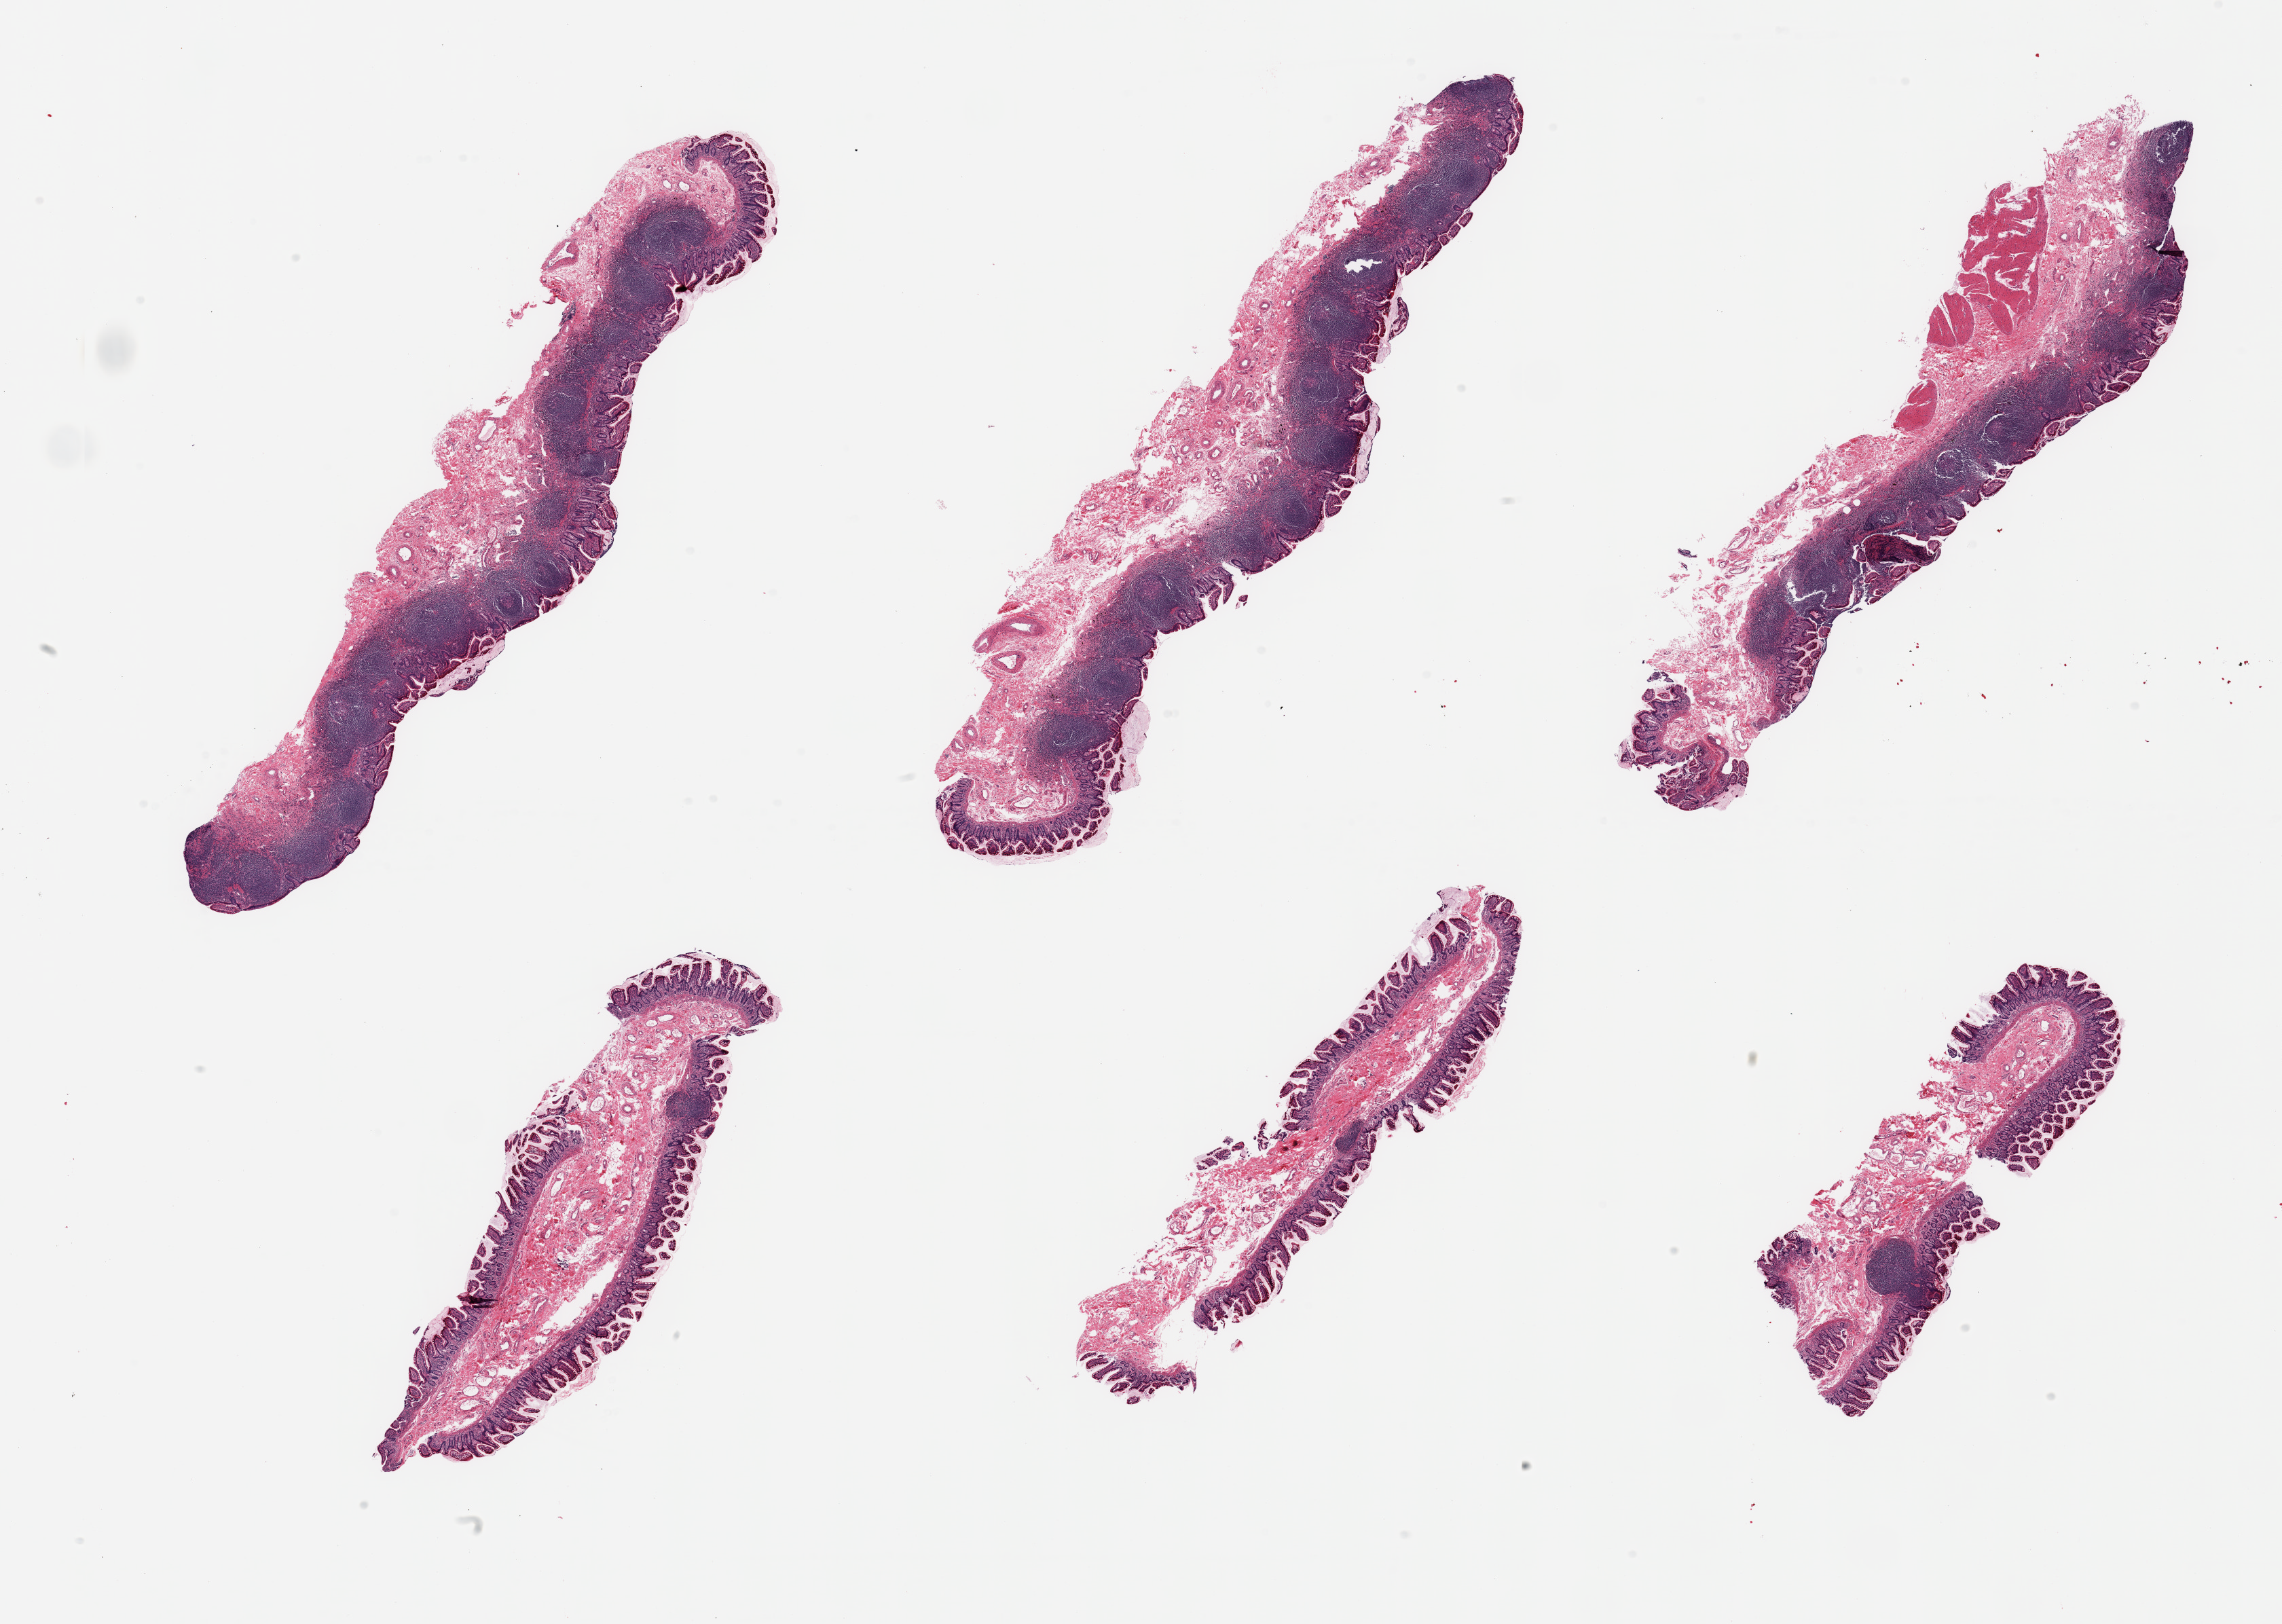
Whole-slide image, haematoxylin and eosin stain, shown as a low-resolution overview of the whole scanned area (about 26.6 x 18.9 mm); PAXgene-fixed paraffin-embedded (PFPE) section; section of ileum (target tissue); donor tissue sample. Female donor.
Reviewer comment on this tissue sample: 6 pieces; 3 of 6 have good lymphoid component, 1 piece includes small portion of muscularis.